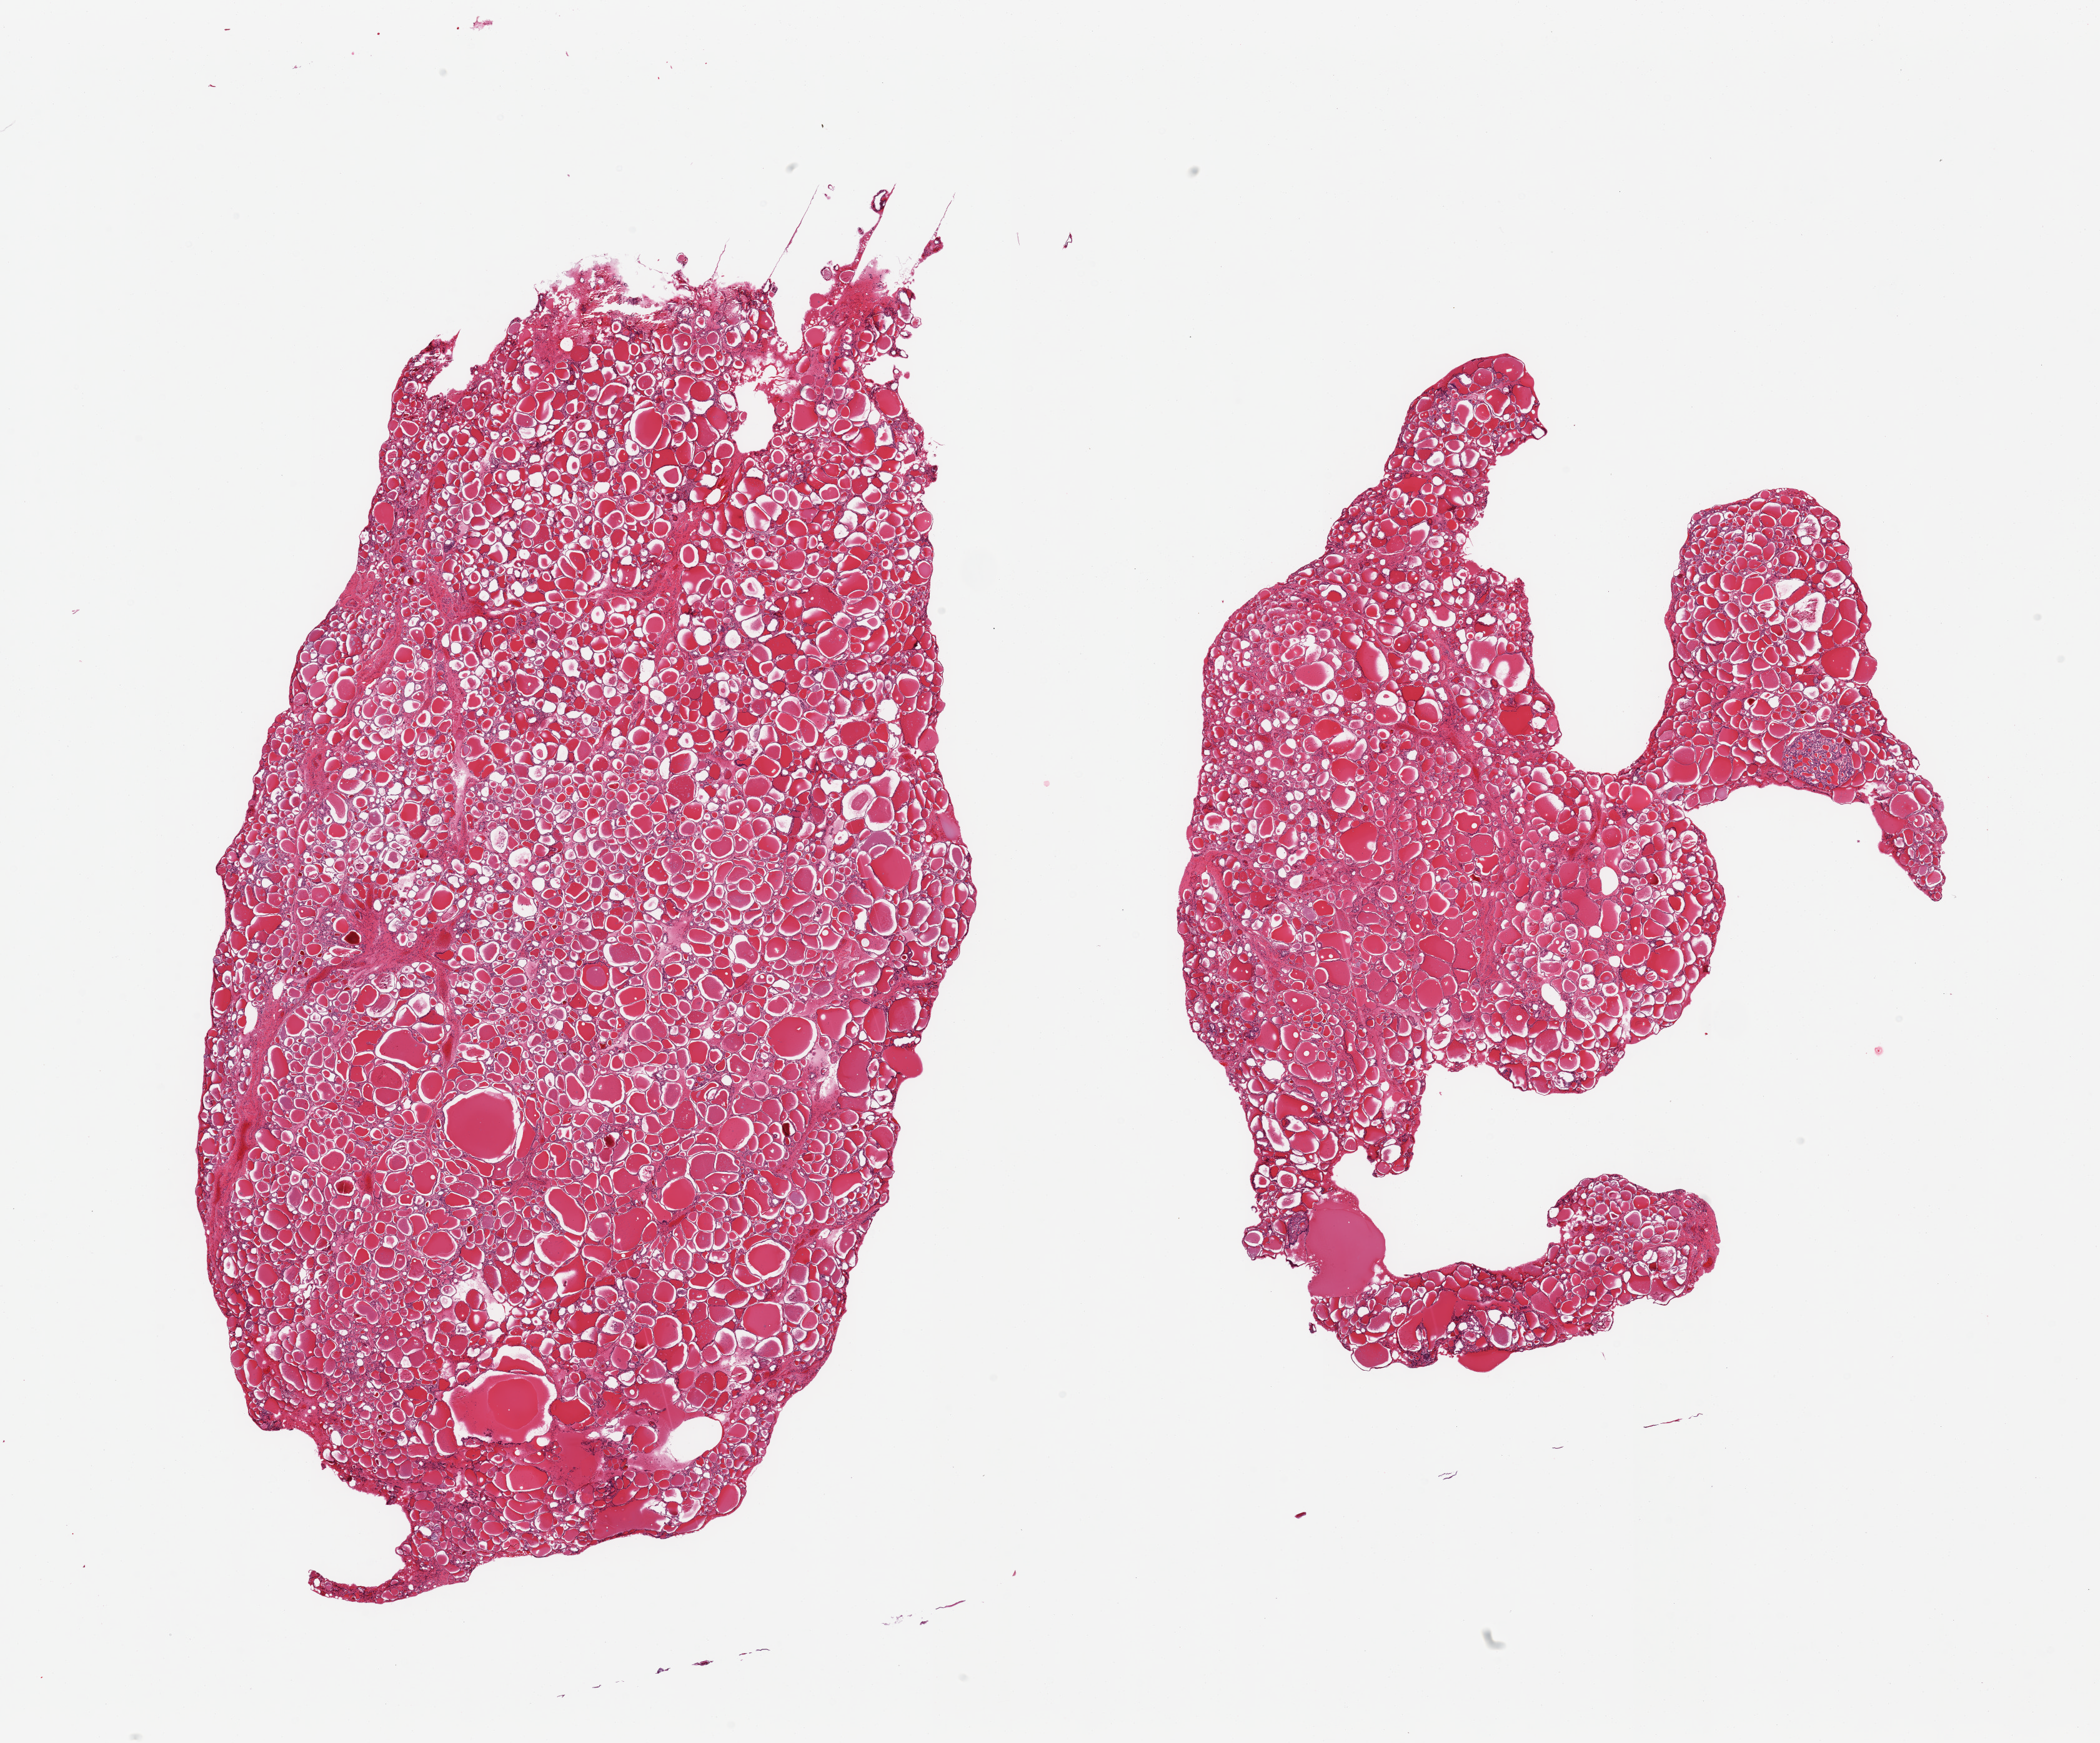
Whole-slide image, haematoxylin and eosin stain, brightfield — a low-resolution overview of the entire scanned area, about 26.6 x 22.1 mm; PAXgene-fixed, paraffin-embedded tissue; section of thyroid (target tissue); tissue donor sample. Donor sex: female.
* pathologist's review note for this sample: 2 pieces, few ~1mm colloid cysts